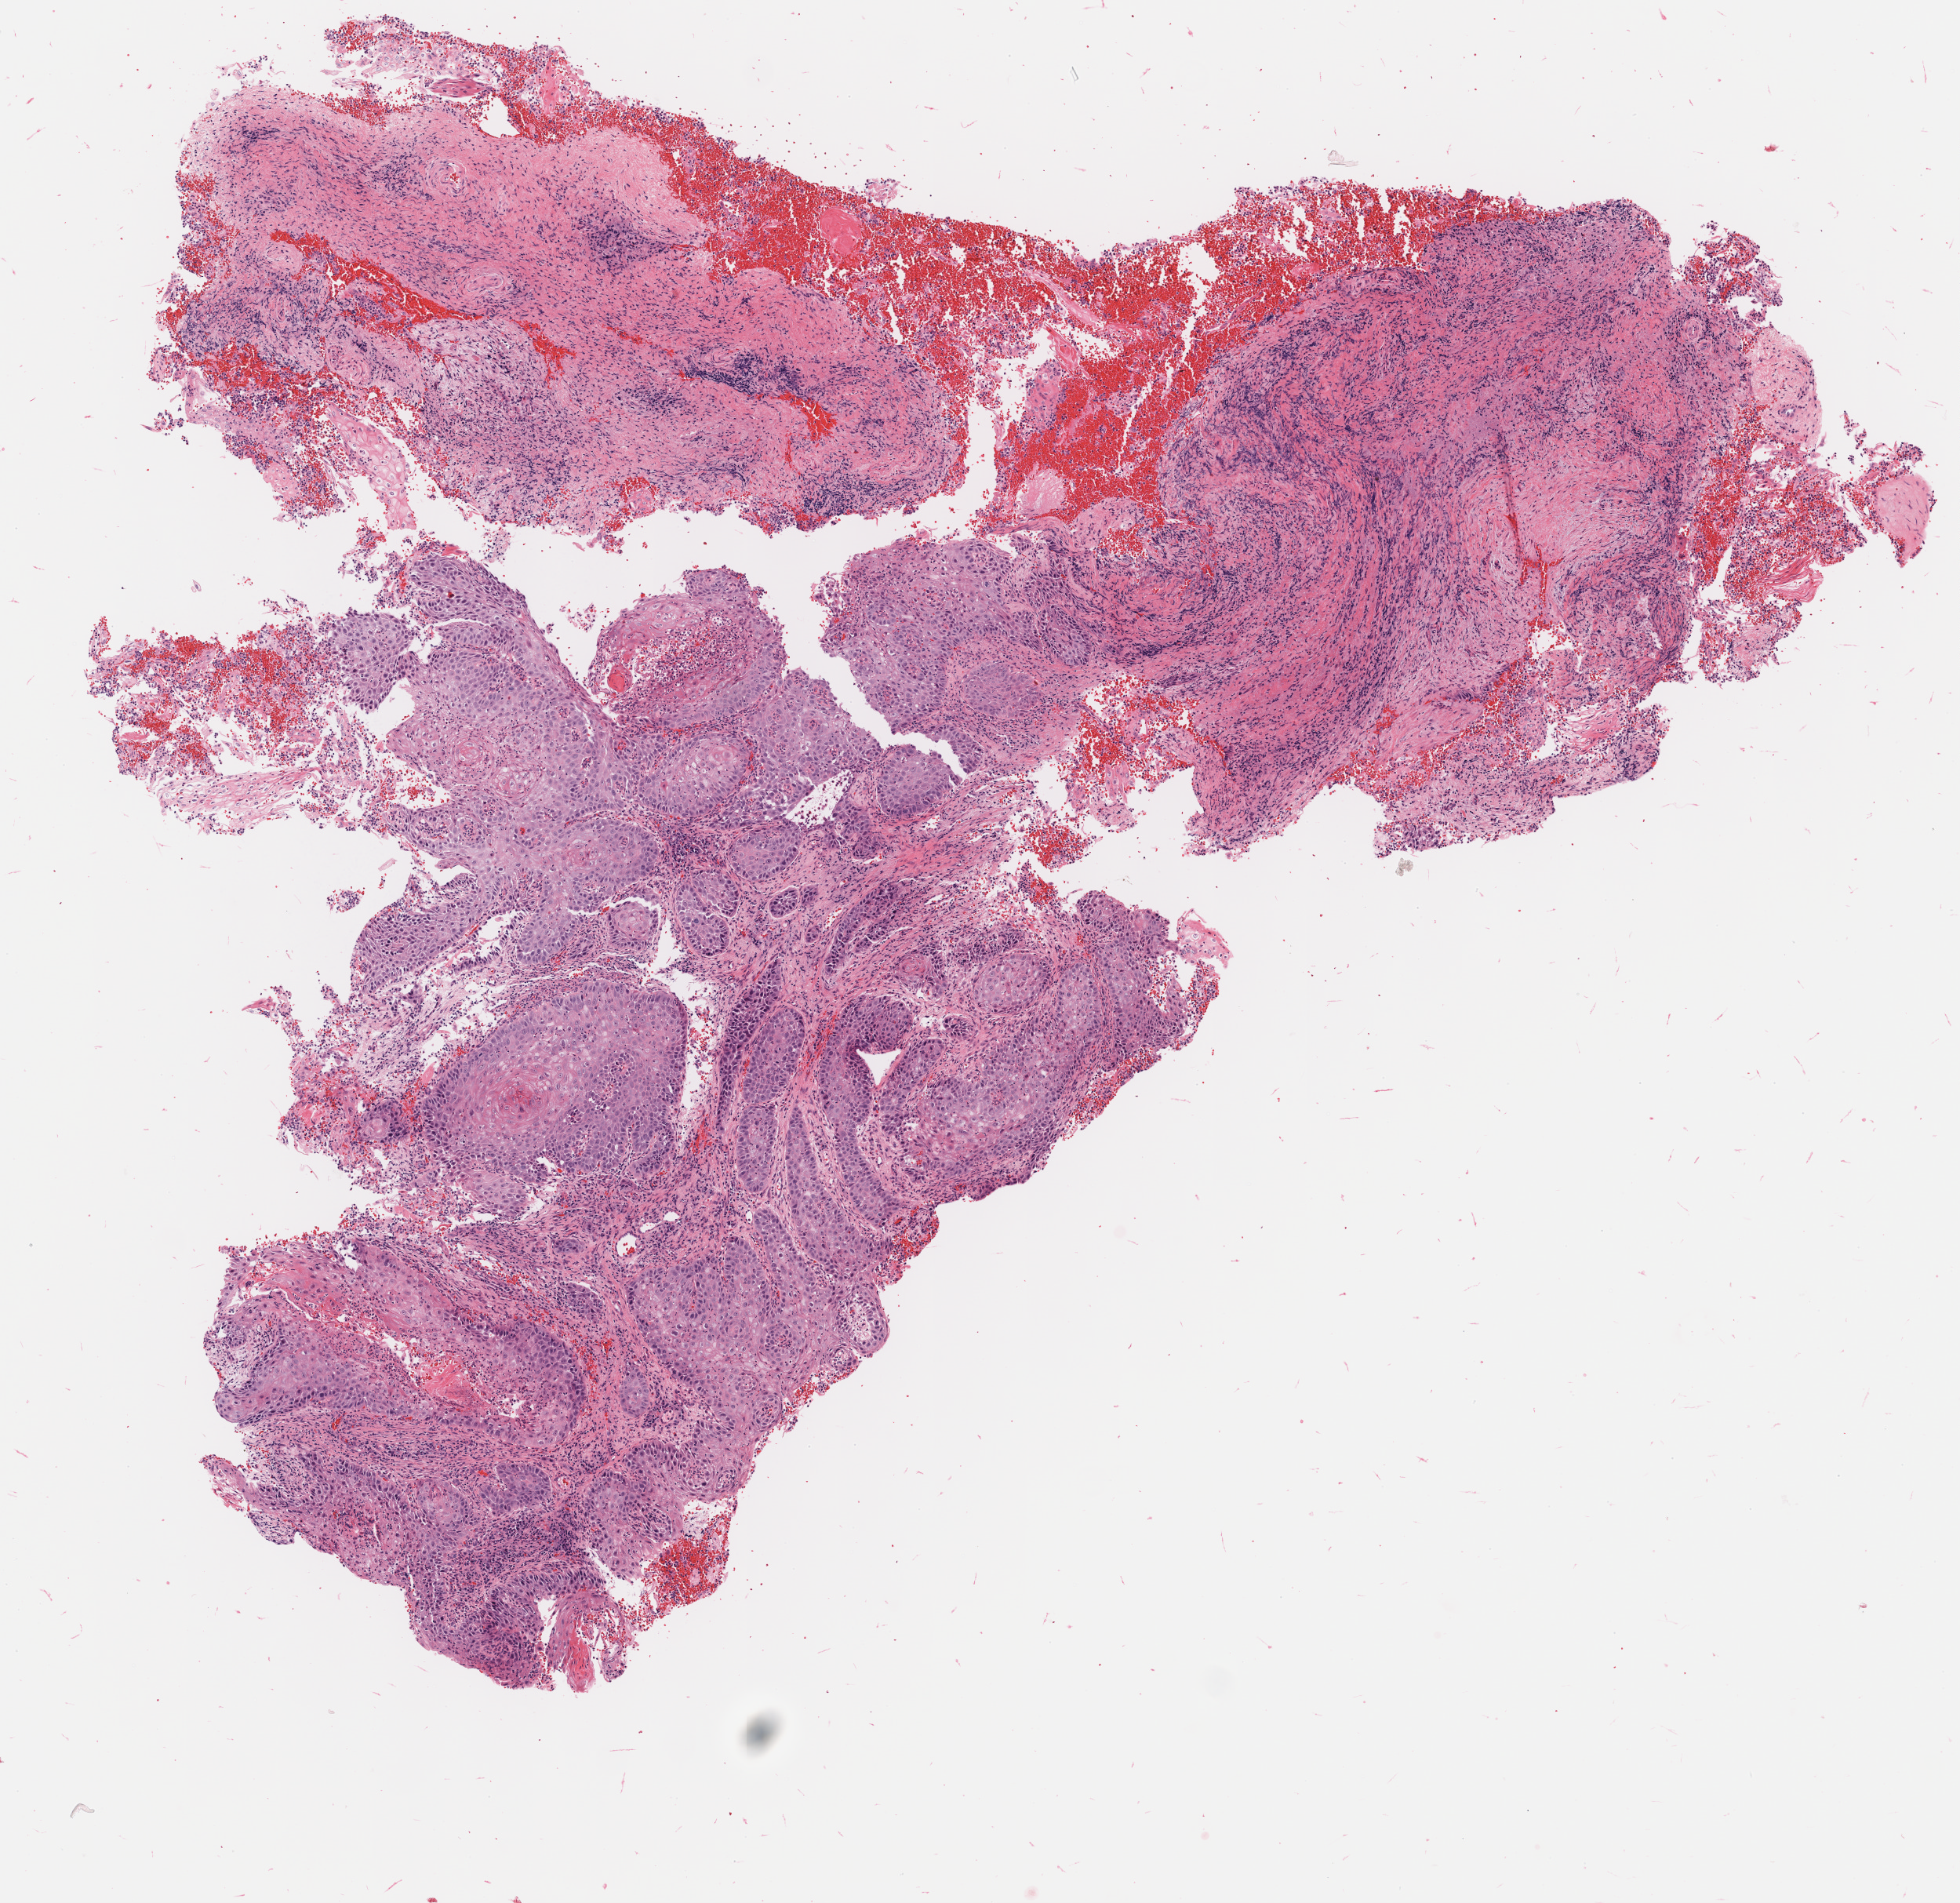
Whole-slide image, H&E stain, low-resolution overview of the scanned area, about 5.0 x 4.8 mm; tumor tissue; site: cervix. Female patient, age 78 years.
Diagnosis: Squamous cell carcinoma, large cell, nonkeratinizing, NOS.